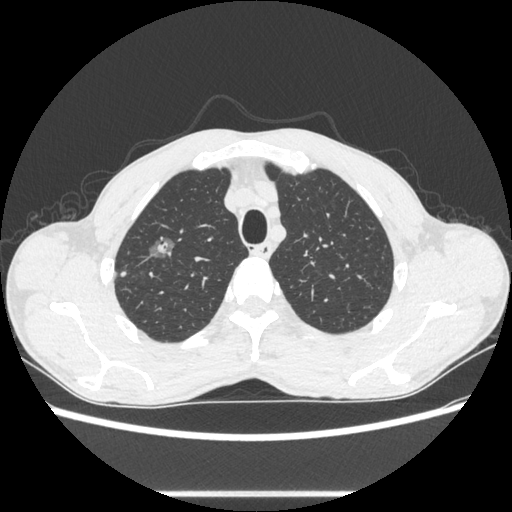
Chest CT, one axial slice; position 487 of 600 along the scan axis; 100 kVp; lung window (W 1500 / L -600 HU); 0.62 mm slice thickness; 512 × 512 image matrix, field of view 357 × 357 mm. Patient: male, 54 years. Case-level facts recorded for this patient, not image findings: clinical TNM (as recorded): T1a N0 M0.
Outlined on this slice (rectangle marked by the reading radiologist):
- lung tumour (recorded histology: adenocarcinoma): bounding box [x1, y1, x2, y2] px = [138, 227, 185, 265]